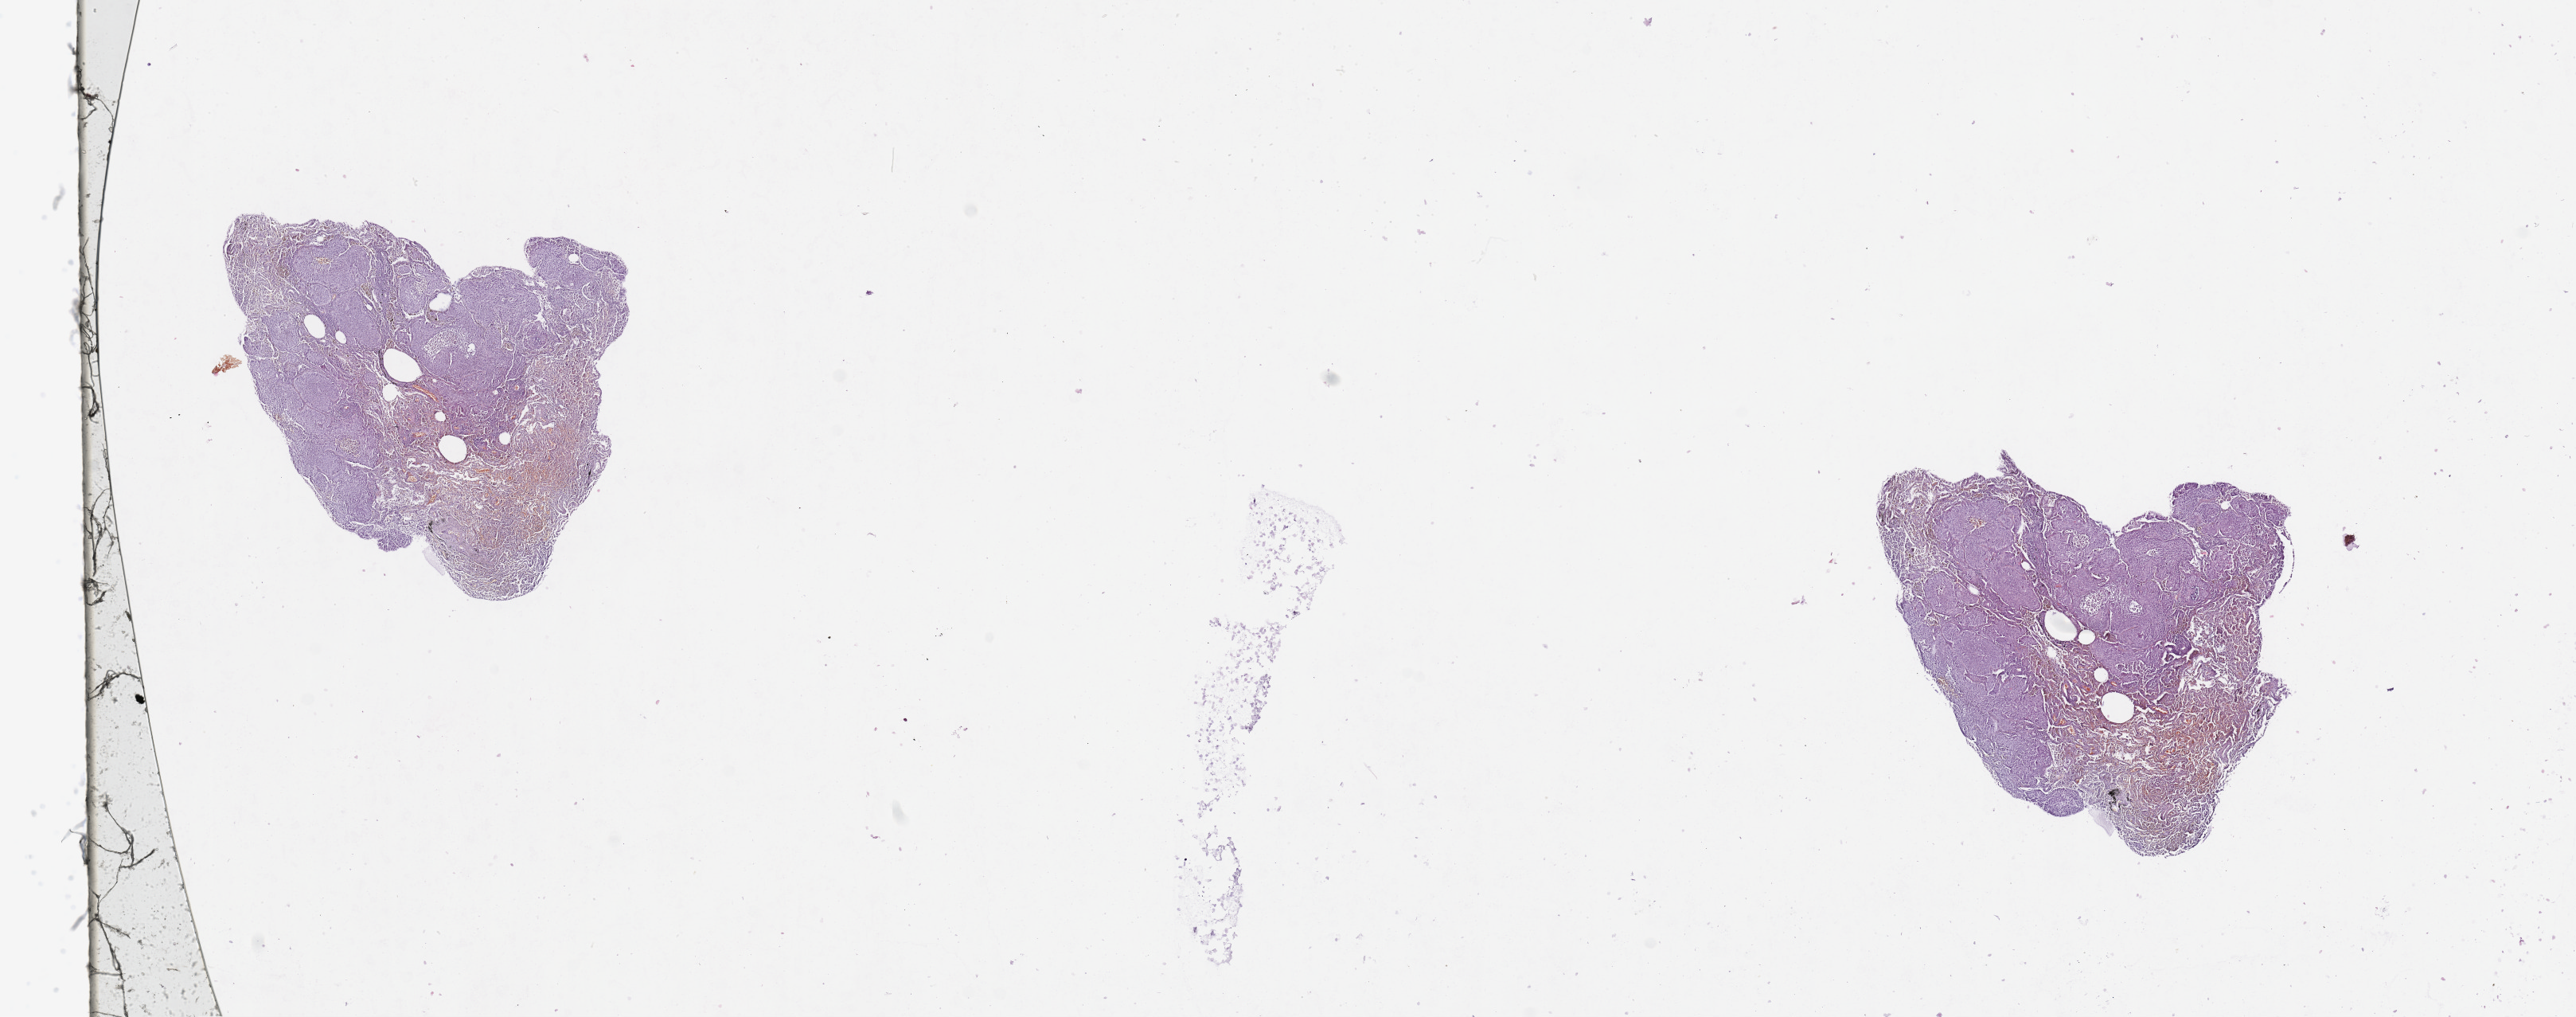
Whole-slide histology image, H&E-stained — whole scanned area (about 25.6 x 10.1 mm, acquisition: 20x scan) shown as a low-resolution overview; tumour tissue sample, sampled site: lung. Patient: male, age 74 years. Histologic grade: G2 (moderately differentiated). Pathologist review of this section (percent, as recorded): tumour nuclei 70%, necrosis 10%.
• diagnosis: Squamous cell carcinoma, NOS
• primary tumour site (as recorded): left lower lobe
• AJCC pathologic stage: IIIA